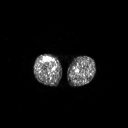
FDG PET of an extremity soft-tissue mass (from a PET/CT study), one axial slice; position 247 of 311 along the scan axis; 128 × 128 image matrix, field of view 700 × 700 mm. Male patient, age 56 years. From the clinical record (not read from this slice): histological type: pleiomorphic leiomyosarcoma; grade: intermediate; site of the primary tumour: right thigh.
Outlined on this slice (expert contour drawn on MRI and transferred to this co-registered scan by the dataset authors):
- gross tumour volume including surrounding oedema: bounding box (x1, y1, x2, y2) in pixels: (44, 56, 51, 62)